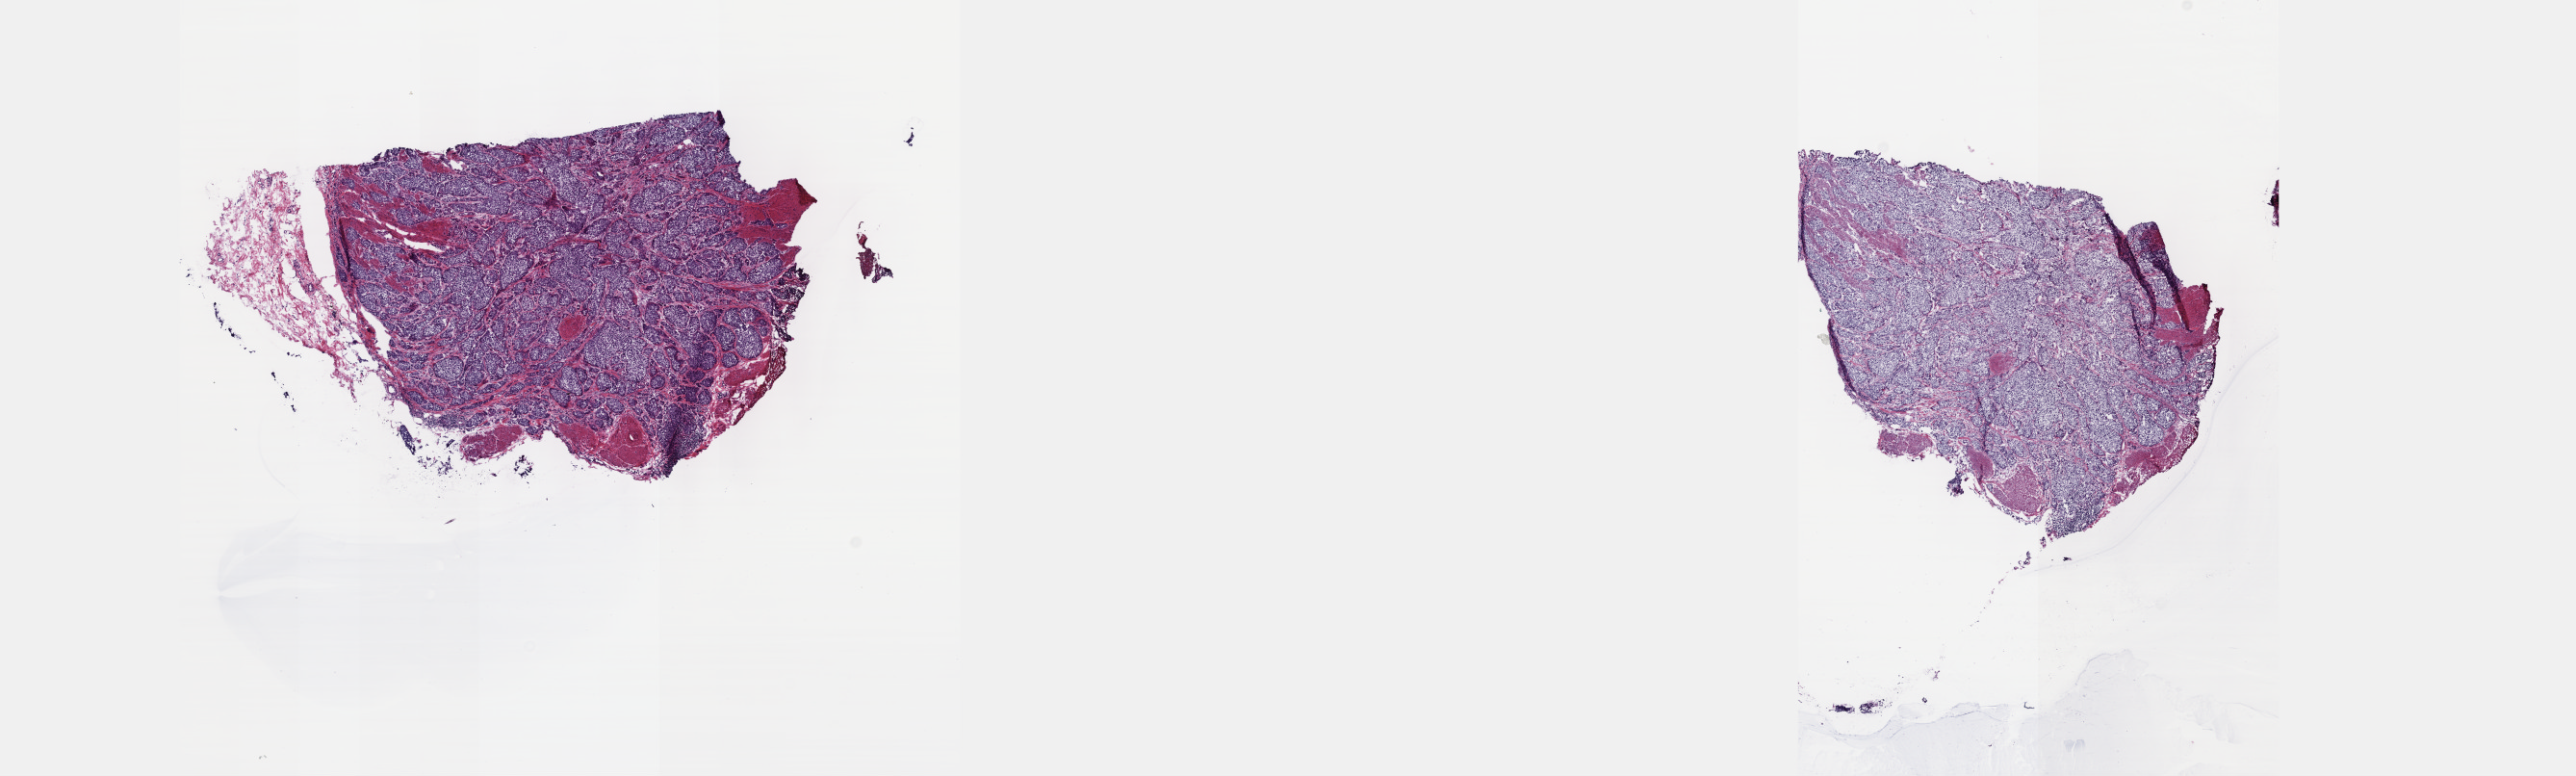
Digitized Hematoxylin and eosin (H&E) stained tissue section (whole slide), a low-resolution overview of the entire scanned area, about 21.6 x 6.5 mm (slide scanned at 40x). Frozen section. Sample: primary tumour, bladder. Male patient; age at initial diagnosis 56 years. Histologic grade: high grade. Composition of this section per pathologist review: tumour cells 100%, tumour nuclei 75%, normal cells 0%, stromal cells 0%, necrosis 0%. Inflammatory infiltration, as recorded: lymphocyte infiltration 2%, monocyte infiltration 0%, neutrophil infiltration 0%.
- pathologic diagnosis: Transitional cell carcinoma (anterior wall of bladder)
- AJCC pathologic stage: III (7th edition)